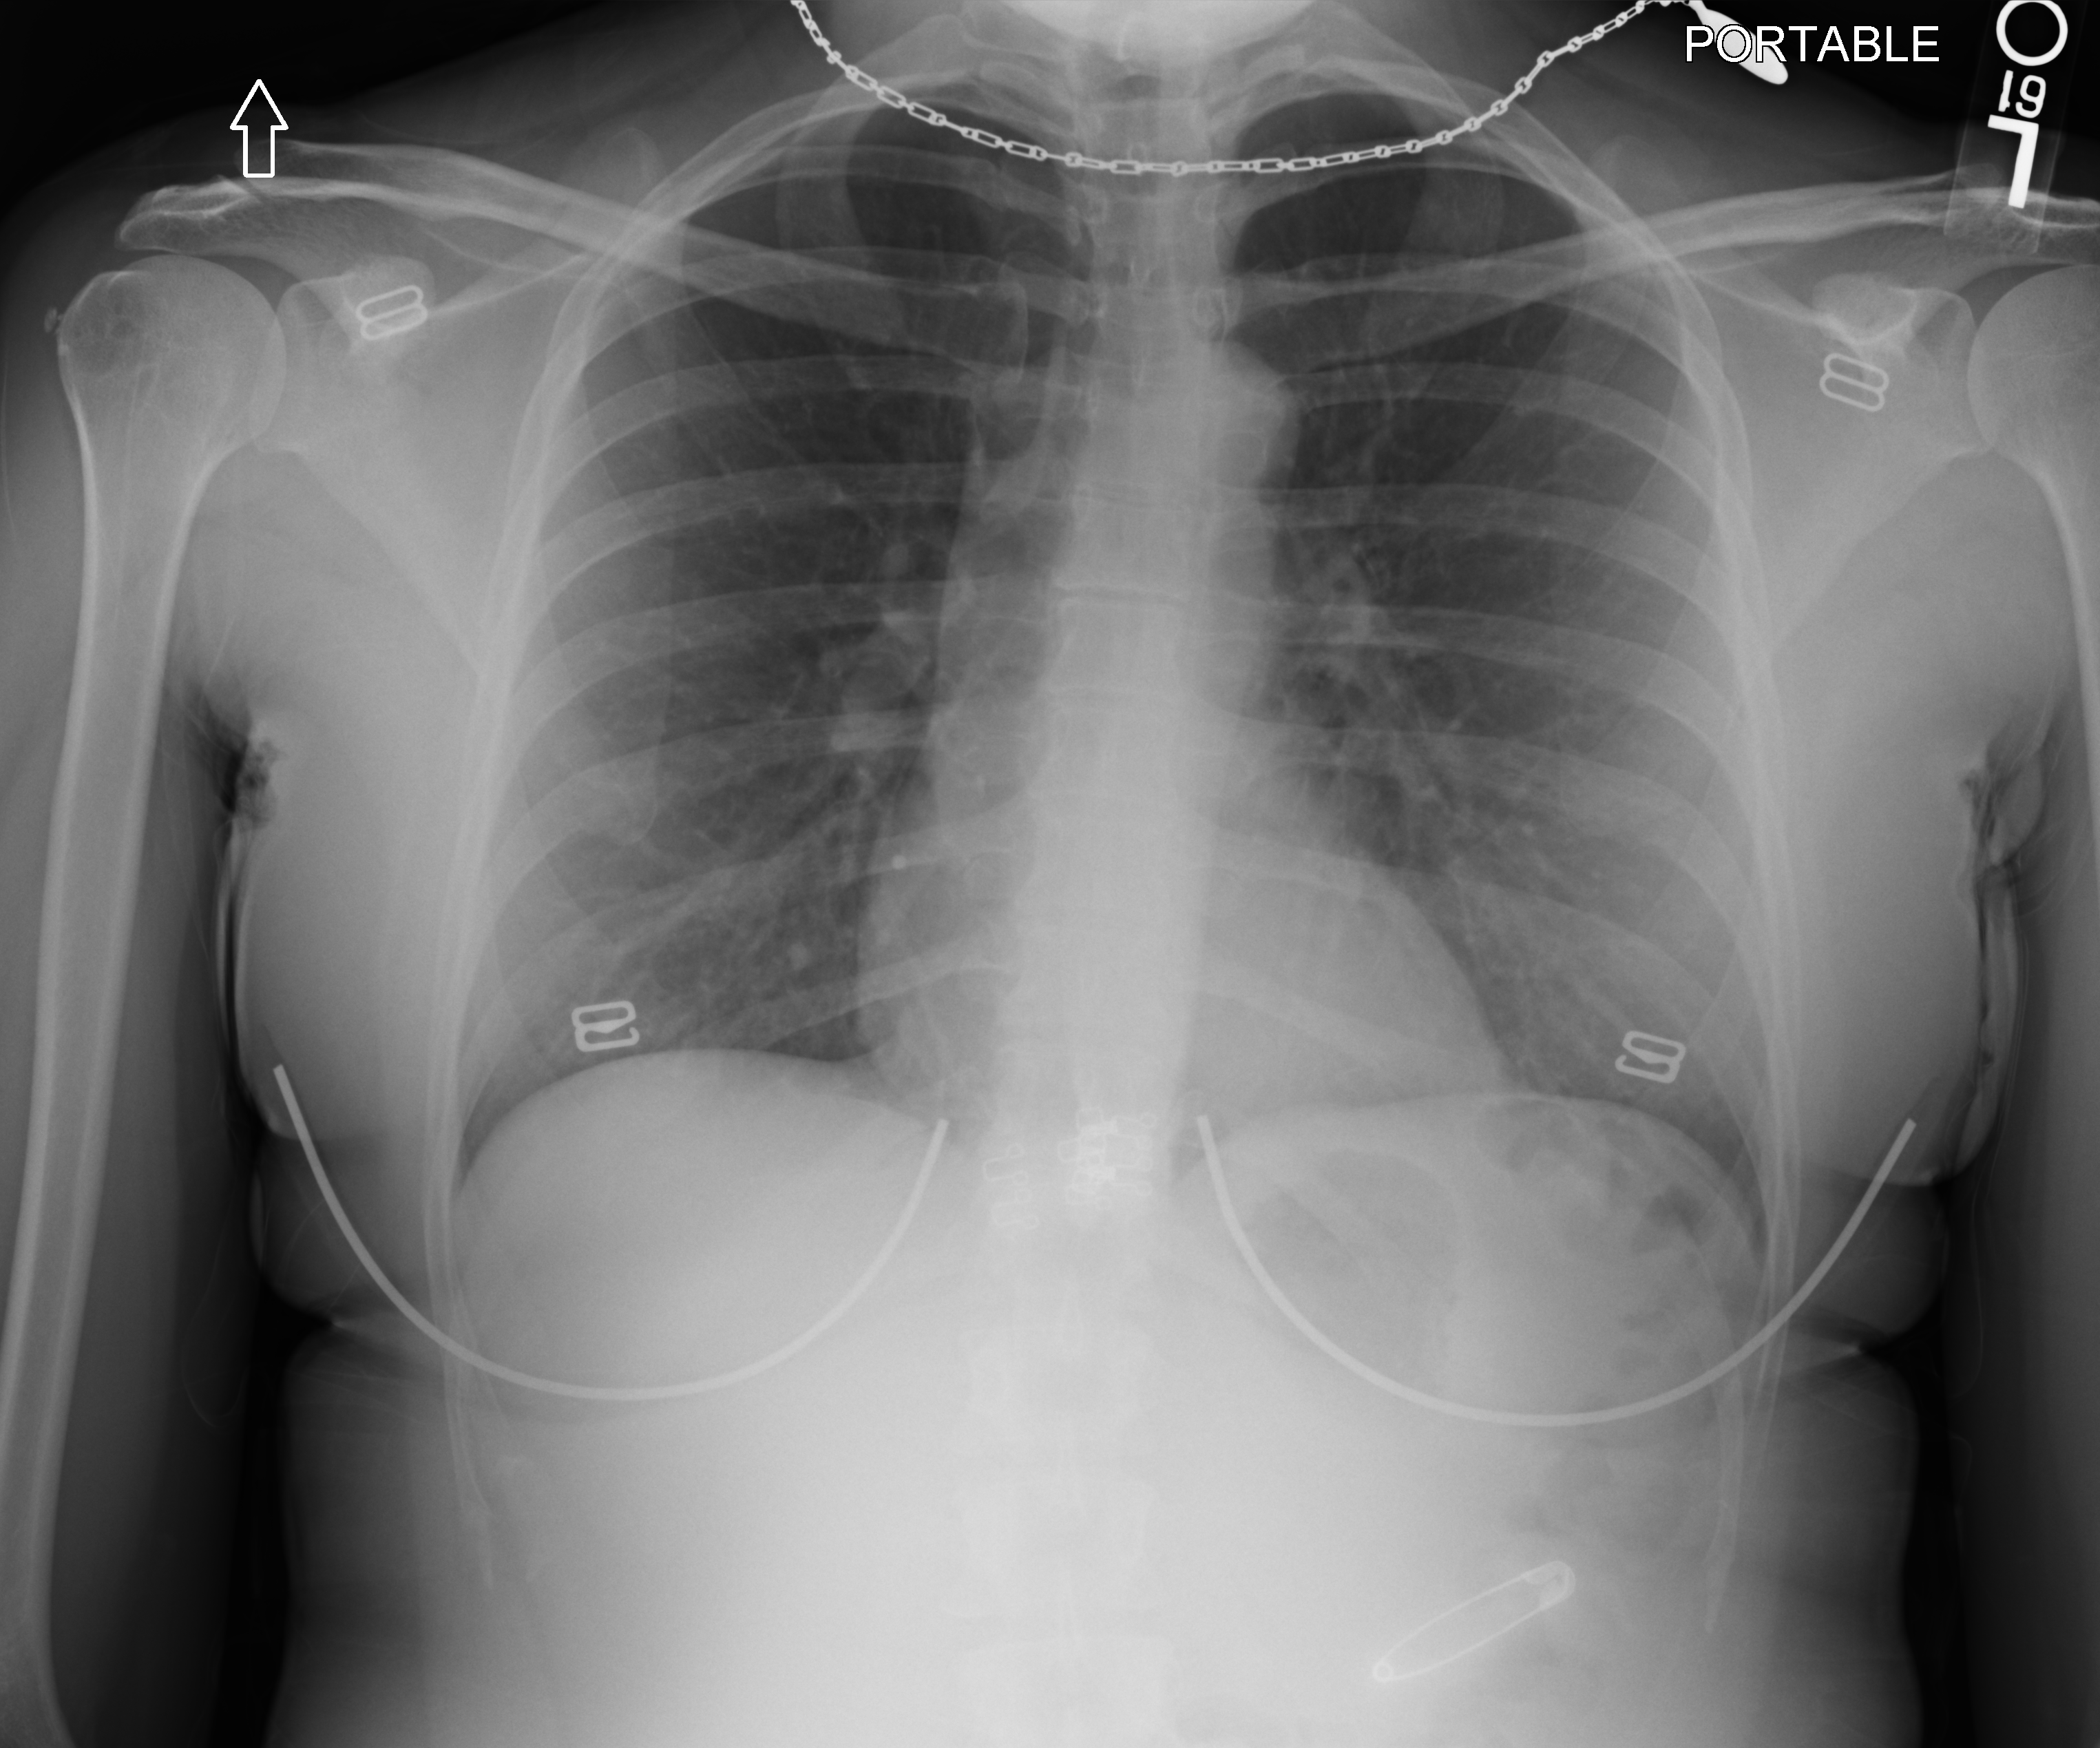
Bedside chest radiograph (computed radiography); anteroposterior (AP) projection. Female patient hospitalised with COVID-19, age 18–59 years.
From the hospital-stay record, not from the radiograph (when in the stay this image was taken is not recorded): admitted to intensive care during this hospital stay: no; length of hospital stay: 1 day.